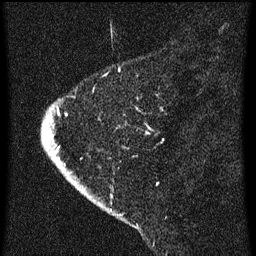
Breast MRI (dynamic contrast-enhanced), one sagittal slice. Slice 12 of 60 in the series (ordered by position). Dynamic contrast-enhanced series, image 2 of 3 at this slice position (ordered by acquisition). 1.5 T. TE 4.2 ms, TR 8 ms. 2 mm slice thickness. 256 × 256 image matrix, field of view 180 × 180 mm. Patient: female, 47 years.
Annotated regions visible in this slice (semi-automatically segmented with operator editing):
- analysis volume of interest (the breast-tissue region the enhancement analysis was run in; not a lesion): box from (x=40, y=80) to (x=164, y=193) px
- tumour enhancement mask (voxels above the 70 % enhancement threshold inside the analysis volume of interest): (x=49, y=106)–(x=150, y=163)